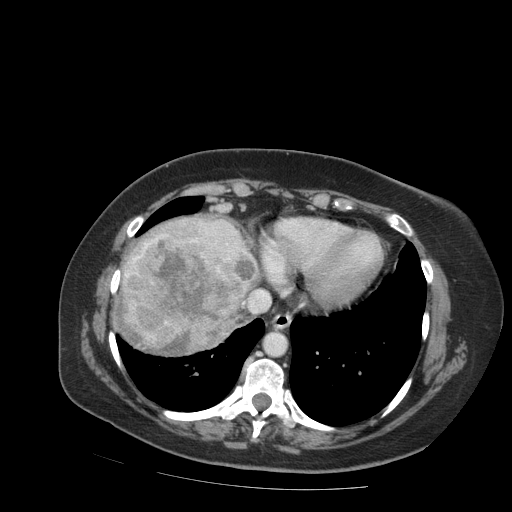
Contrast-enhanced abdominal CT (liver protocol), one axial slice; slice 80 of 99 in the series (ordered by position); soft-tissue window (W 400 / L 40 HU); 512 × 512 image matrix, field of view 400 × 400 mm. From the clinical record (not read from this slice): diagnosis: hepatocellular carcinoma (patient treated with transarterial chemoembolisation; whether this scan precedes or follows treatment is not stated here); TNM stage (as recorded): Stage-IVB; Child-Pugh class: A; tumour differentiation: moderately differentiated; tumour nodularity: uninodular.
Outlined on this slice (semi-automatic segmentation, software-assisted and operator-edited):
- liver parenchyma outside the tumour (the mass and vessels are separate outlines, so this box may not span the whole liver): bounding box (x1, y1, x2, y2) in pixels: (120, 216, 258, 348)
- mass: (115, 236, 255, 357)
- liver vessels: (163, 224, 239, 260)